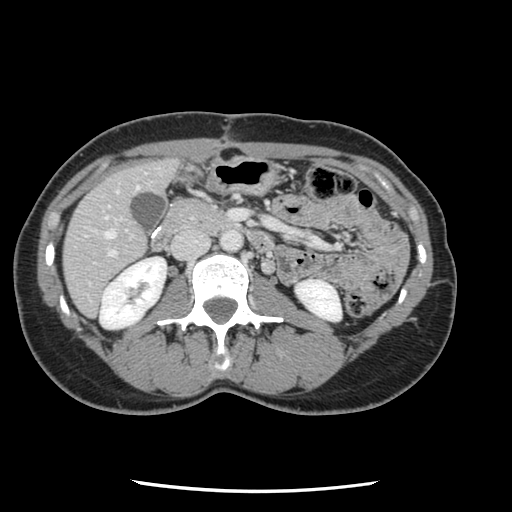
Contrast-enhanced abdominal CT, one axial slice; slice 35 of 134 in the series (ordered by position); 120 kVp; intravenous contrast given; soft-tissue window (W 400 / L 40 HU); 2.5 mm slice thickness; 512 × 512 image matrix, field of view 330 × 330 mm. Female patient, age 43 years. Case-level facts recorded for this patient, not image findings: diagnosis: colorectal cancer liver metastases, imaged before liver resection; multiple liver metastases: yes; largest metastasis: 3.4 cm; disease in both lobes: yes.
Structures marked on this image (outlined manually by an expert reader):
- hepatic veins: bounding box [x1, y1, x2, y2] px = [105, 187, 138, 239]
- liver: [65, 160, 177, 316]
- planned liver remnant (the part of the liver to remain after resection): [64, 160, 177, 316]